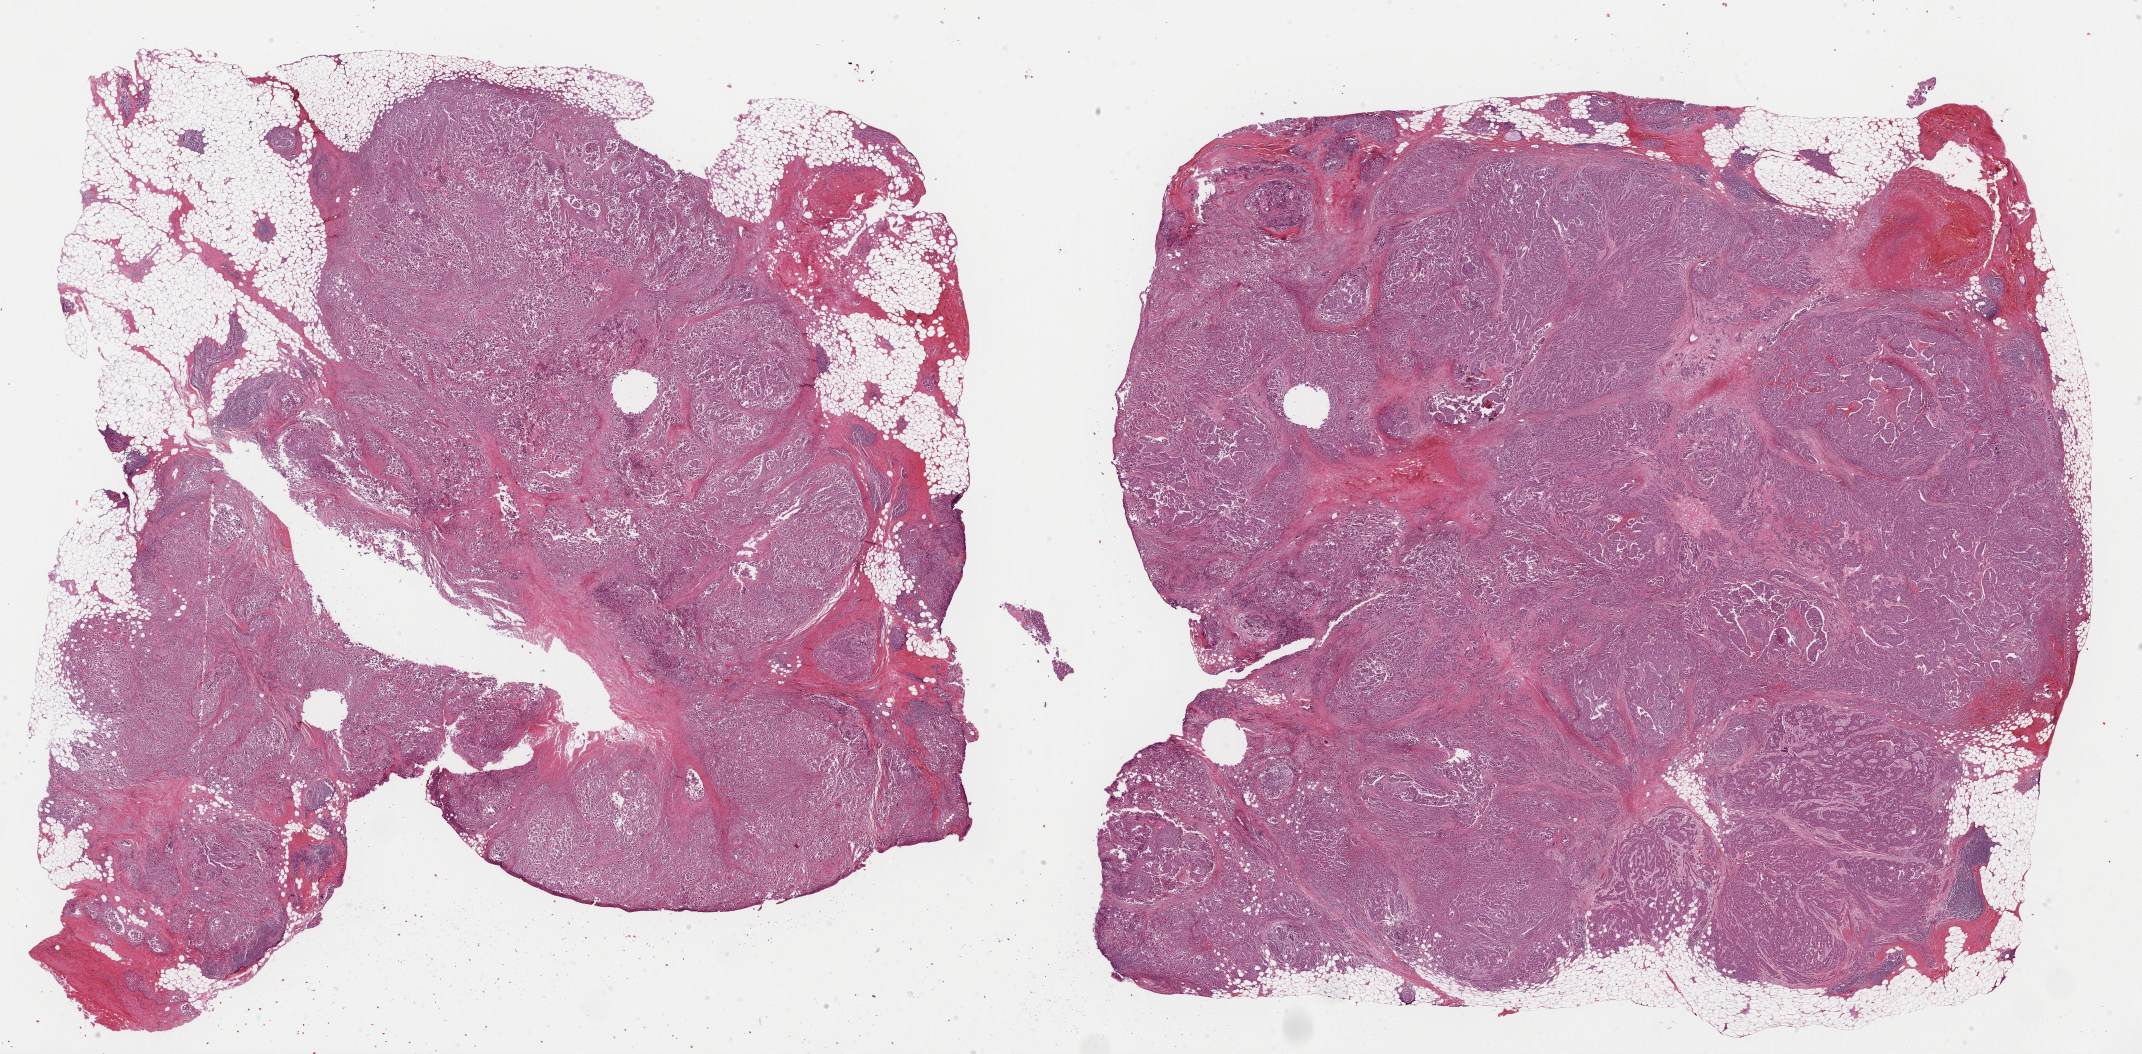
H&E-stained whole-slide image — whole scanned area (about 33.8 x 16.6 mm, from a 40x scan) shown as a low-resolution overview. Formalin-fixed paraffin-embedded (FFPE) diagnostic section. Sample: primary tumour, breast. Patient: female, age at initial diagnosis 59 years.
- AJCC pathologic stage: IIB
- laterality: left
- TNM: T2 N1 M0
- diagnosis: Infiltrating duct carcinoma, NOS
- lymph nodes positive (case pathology): 1 of 4 examined